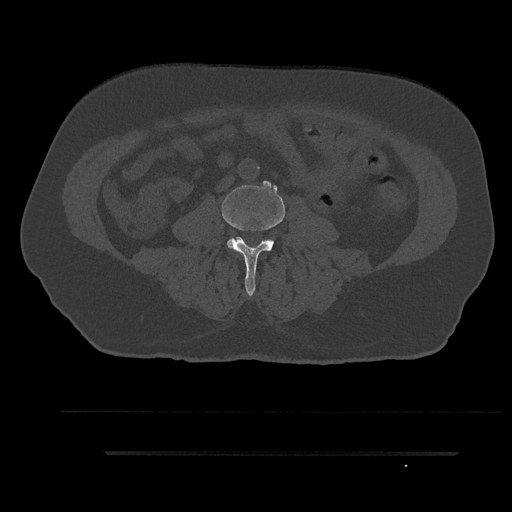
CT including the spine, one axial slice; reconstruction kernel Br40s/3; bone window (W 1800 / L 400 HU); 0.5 mm slice thickness; 512 × 512 image matrix. Male patient, age 63 years. Case-level facts recorded for this patient, not image findings: primary cancer: renal.
Outlined on this slice (semi-automatic segmentation, software-assisted and operator-edited):
- L3 vertebra: bounding box [x1, y1, x2, y2] px = [222, 185, 285, 296]
- L4 vertebra: [268, 239, 274, 245]